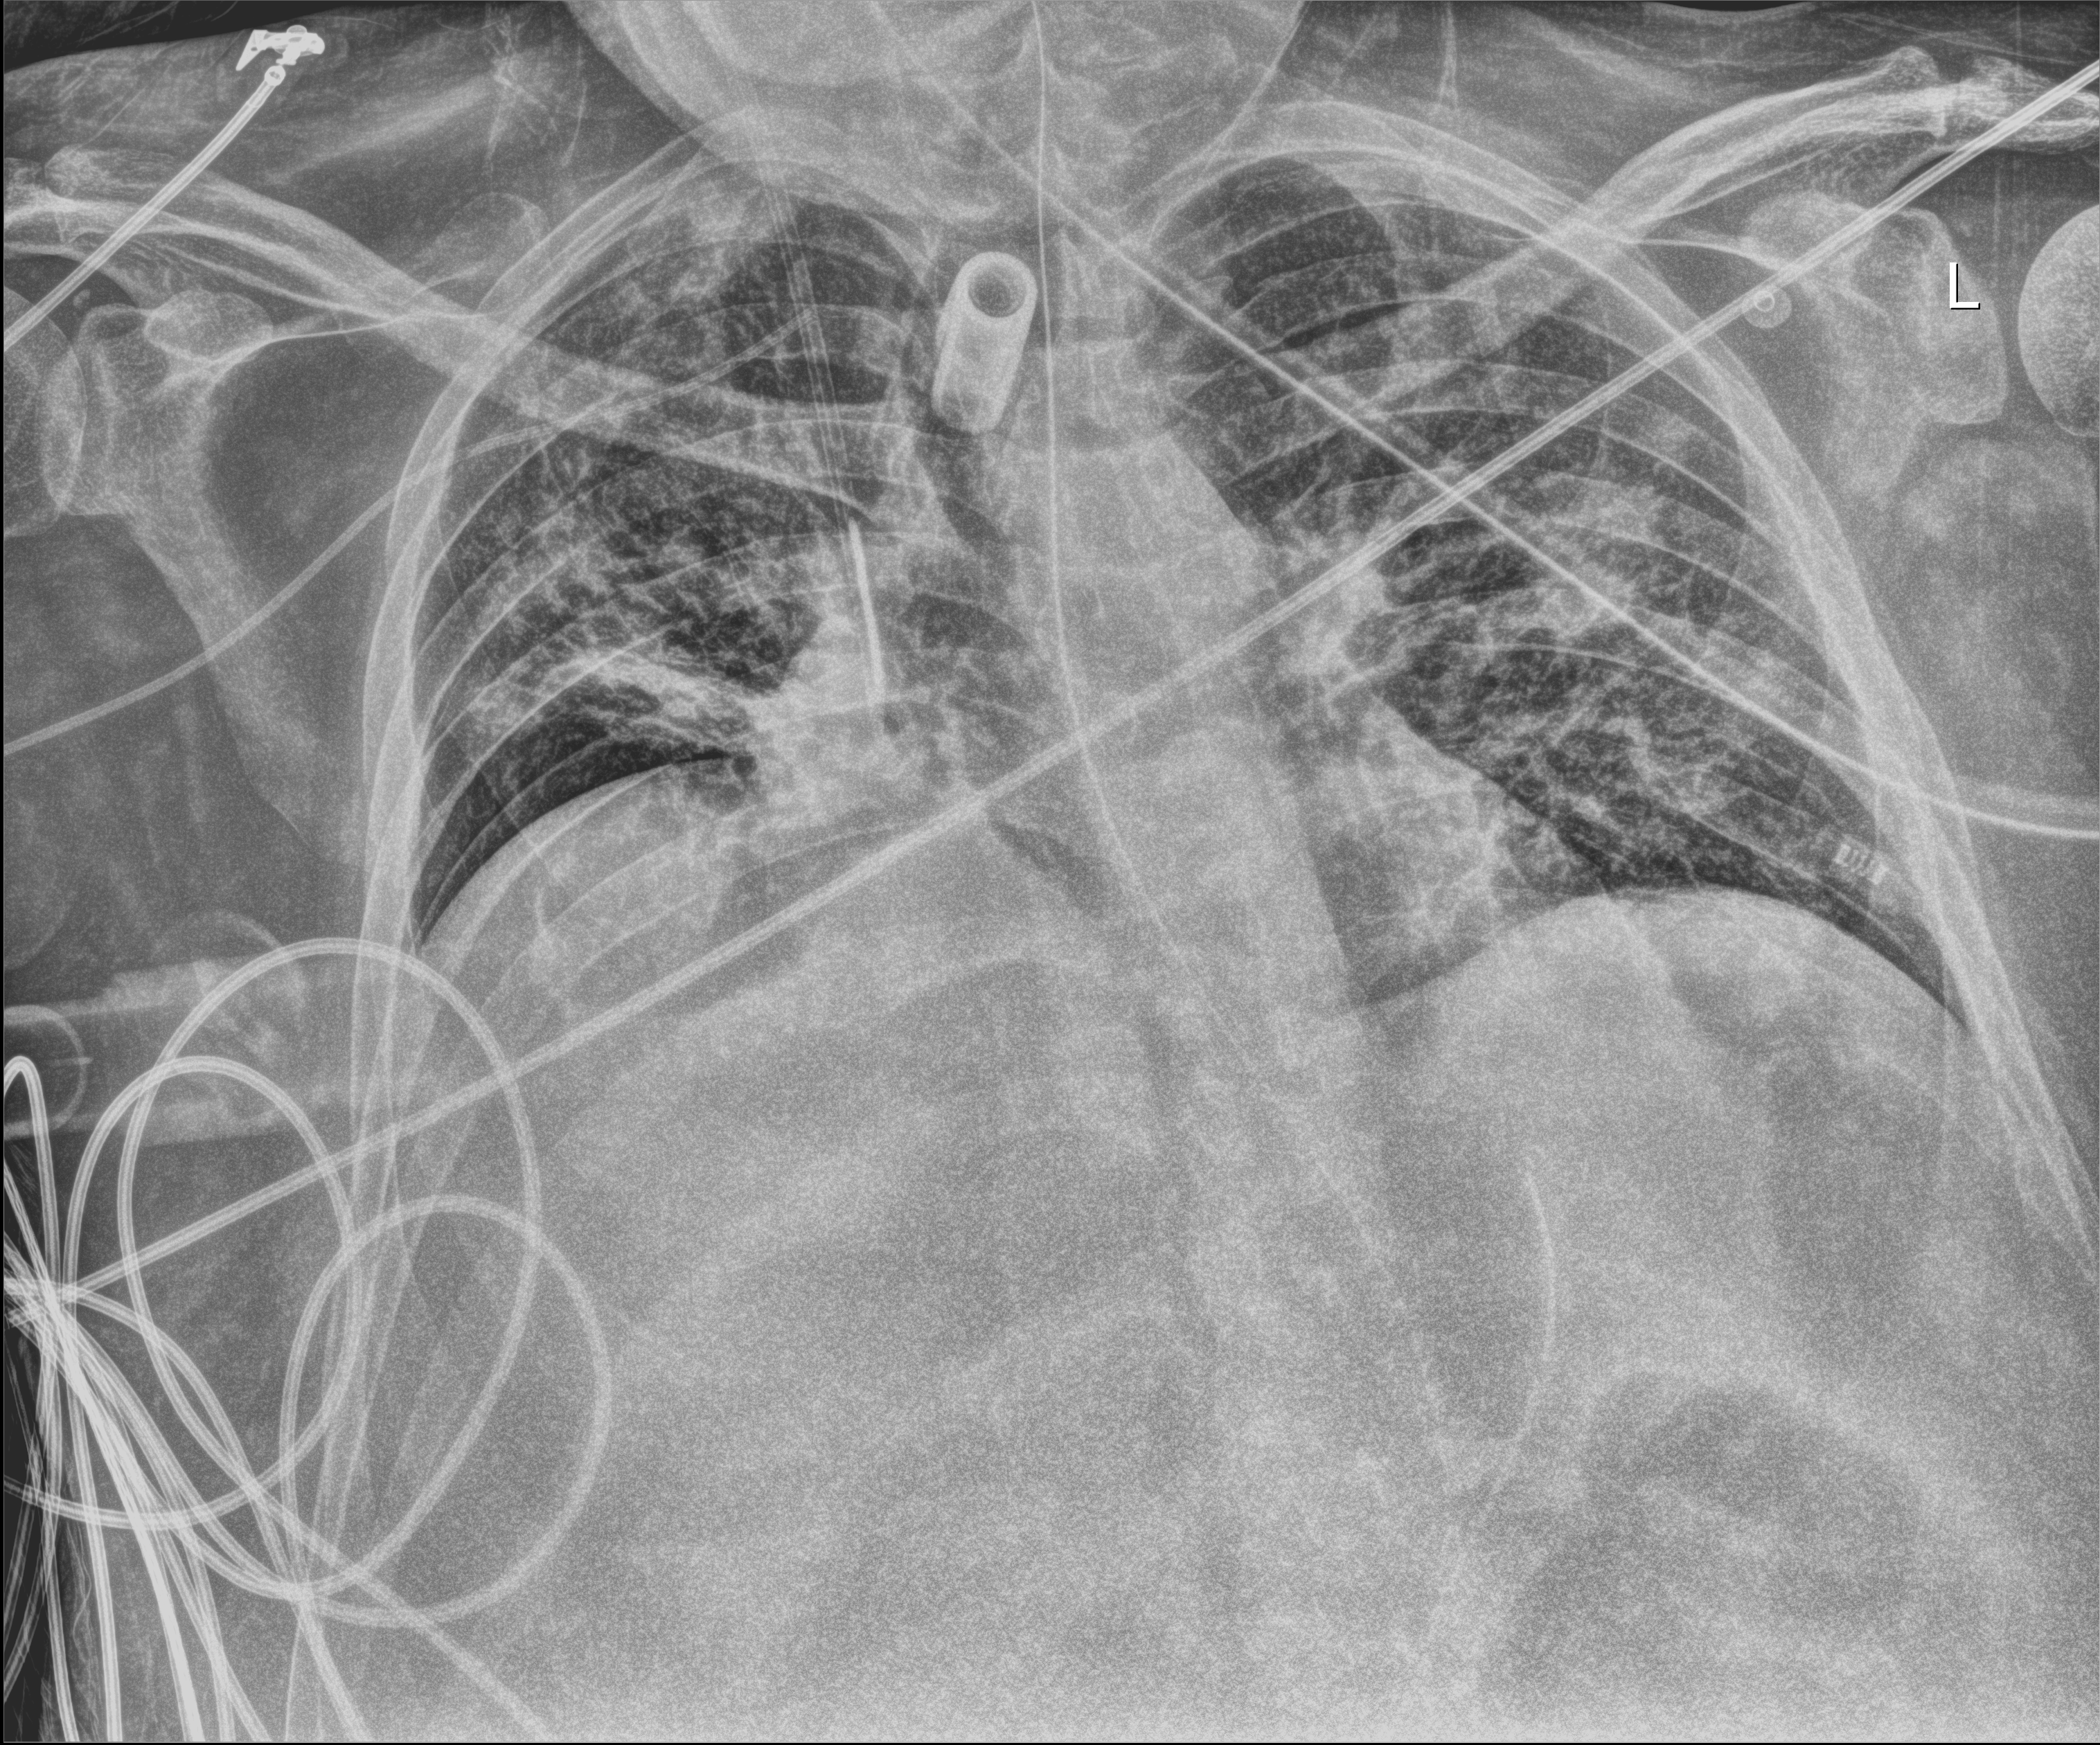
Portable chest radiograph; anteroposterior (AP) projection. Patient hospitalised with COVID-19, aged 18–59 years.
Hospital-stay facts (about this admission, not read from this image; timing relative to this image not recorded):
- mechanically ventilated during this hospital stay: yes